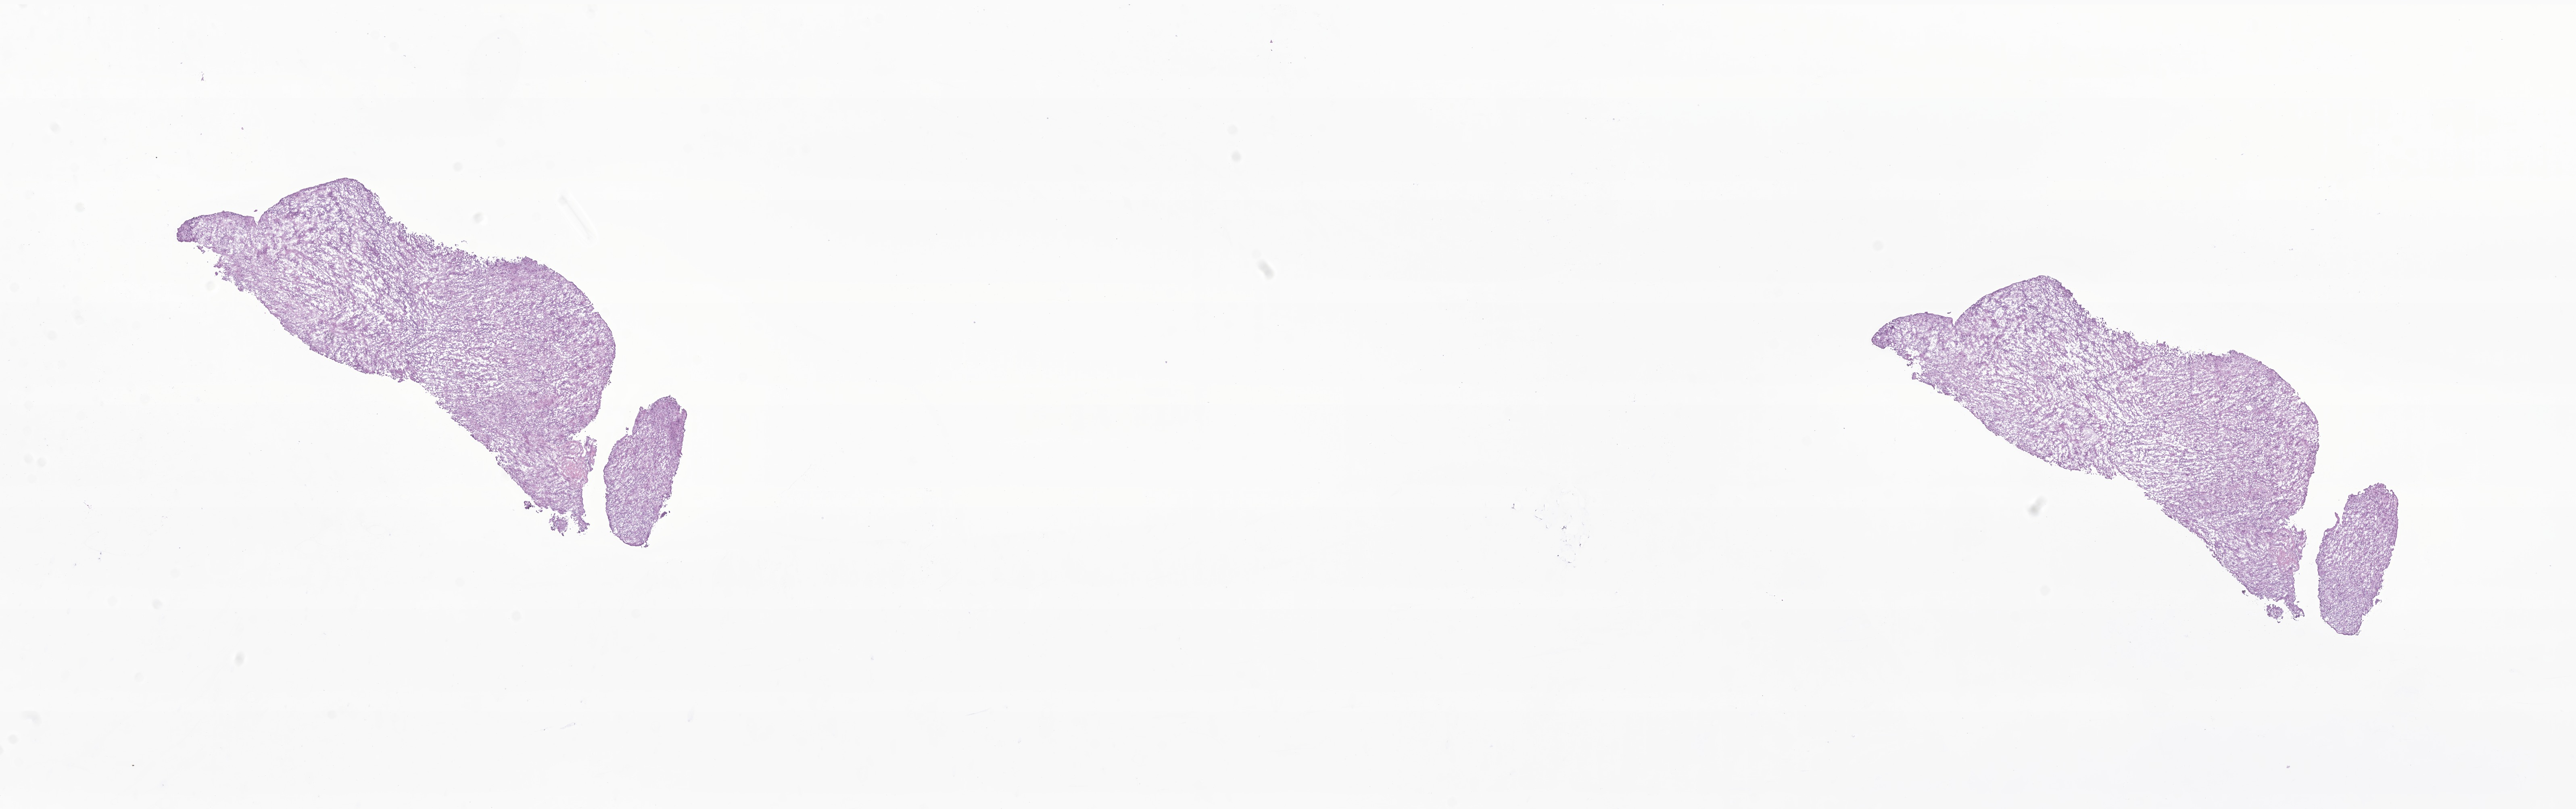
Haematoxylin and eosin whole-slide image of tumor tissue from the brain, whole scanned area (about 26.9 x 8.5 mm) shown as a low-resolution overview; frozen section. Patient female; age 201 months.
Diagnosis (ICD-O-3 morphology term): Ependymoma, NOS.